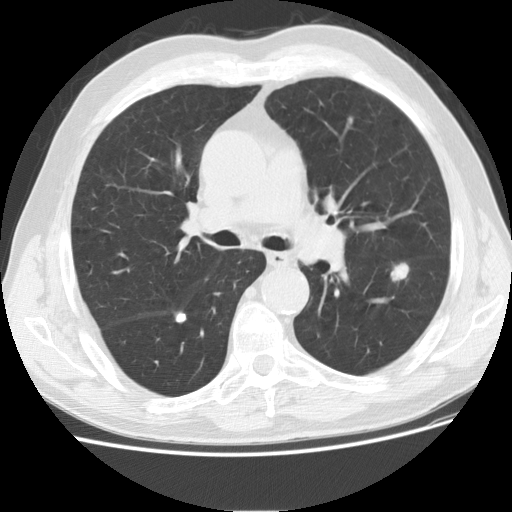
Low-dose screening chest CT, one axial slice; position 111 of 175 along the scan axis; reconstruction kernel STANDARD; lung window (W 1500 / L -600 HU); 2.5 mm slice thickness; 512 × 512 image matrix.
Outlined on this slice (expert manual segmentation):
- lesion 1 (tumor, lower lobe of left lung): bounding box <391,263,409,281> (left, top, right, bottom; pixels)